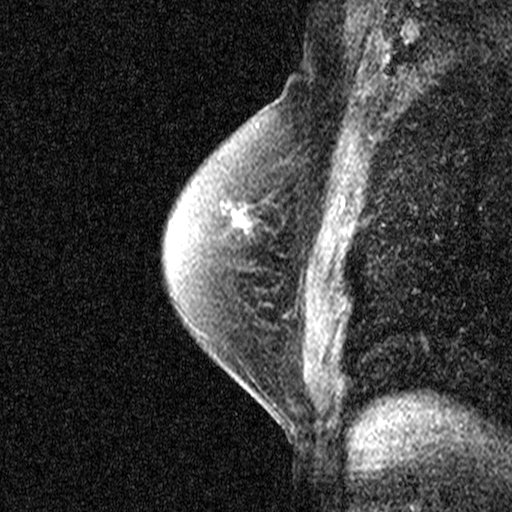
Breast MRI (dynamic contrast-enhanced), one sagittal slice; slice 28 of 40 in the series (ordered by position); dynamic contrast-enhanced study with each time point stored as its own series, time point 2 of 3 at this slice position (early post-contrast, ordered by acquisition time); 1.5 T; TE 4.5 ms, TR 11 ms; 3 mm slice thickness; 512 × 512 image matrix. Patient: female, 55 years. From the clinical record (not read from this slice): setting: breast cancer imaged before/during neoadjuvant chemotherapy; receptor status: HR-positive, HER2-negative.
Structures marked on this image (semi-automatic segmentation, software-assisted and operator-edited):
- analysis volume of interest (the breast-tissue region the enhancement analysis was run in; not a lesion): bounding box <194,202,279,277> (left, top, right, bottom; pixels)
- tumour enhancement mask (voxels above the 90 % enhancement threshold inside the analysis volume of interest): <233,212,242,222>